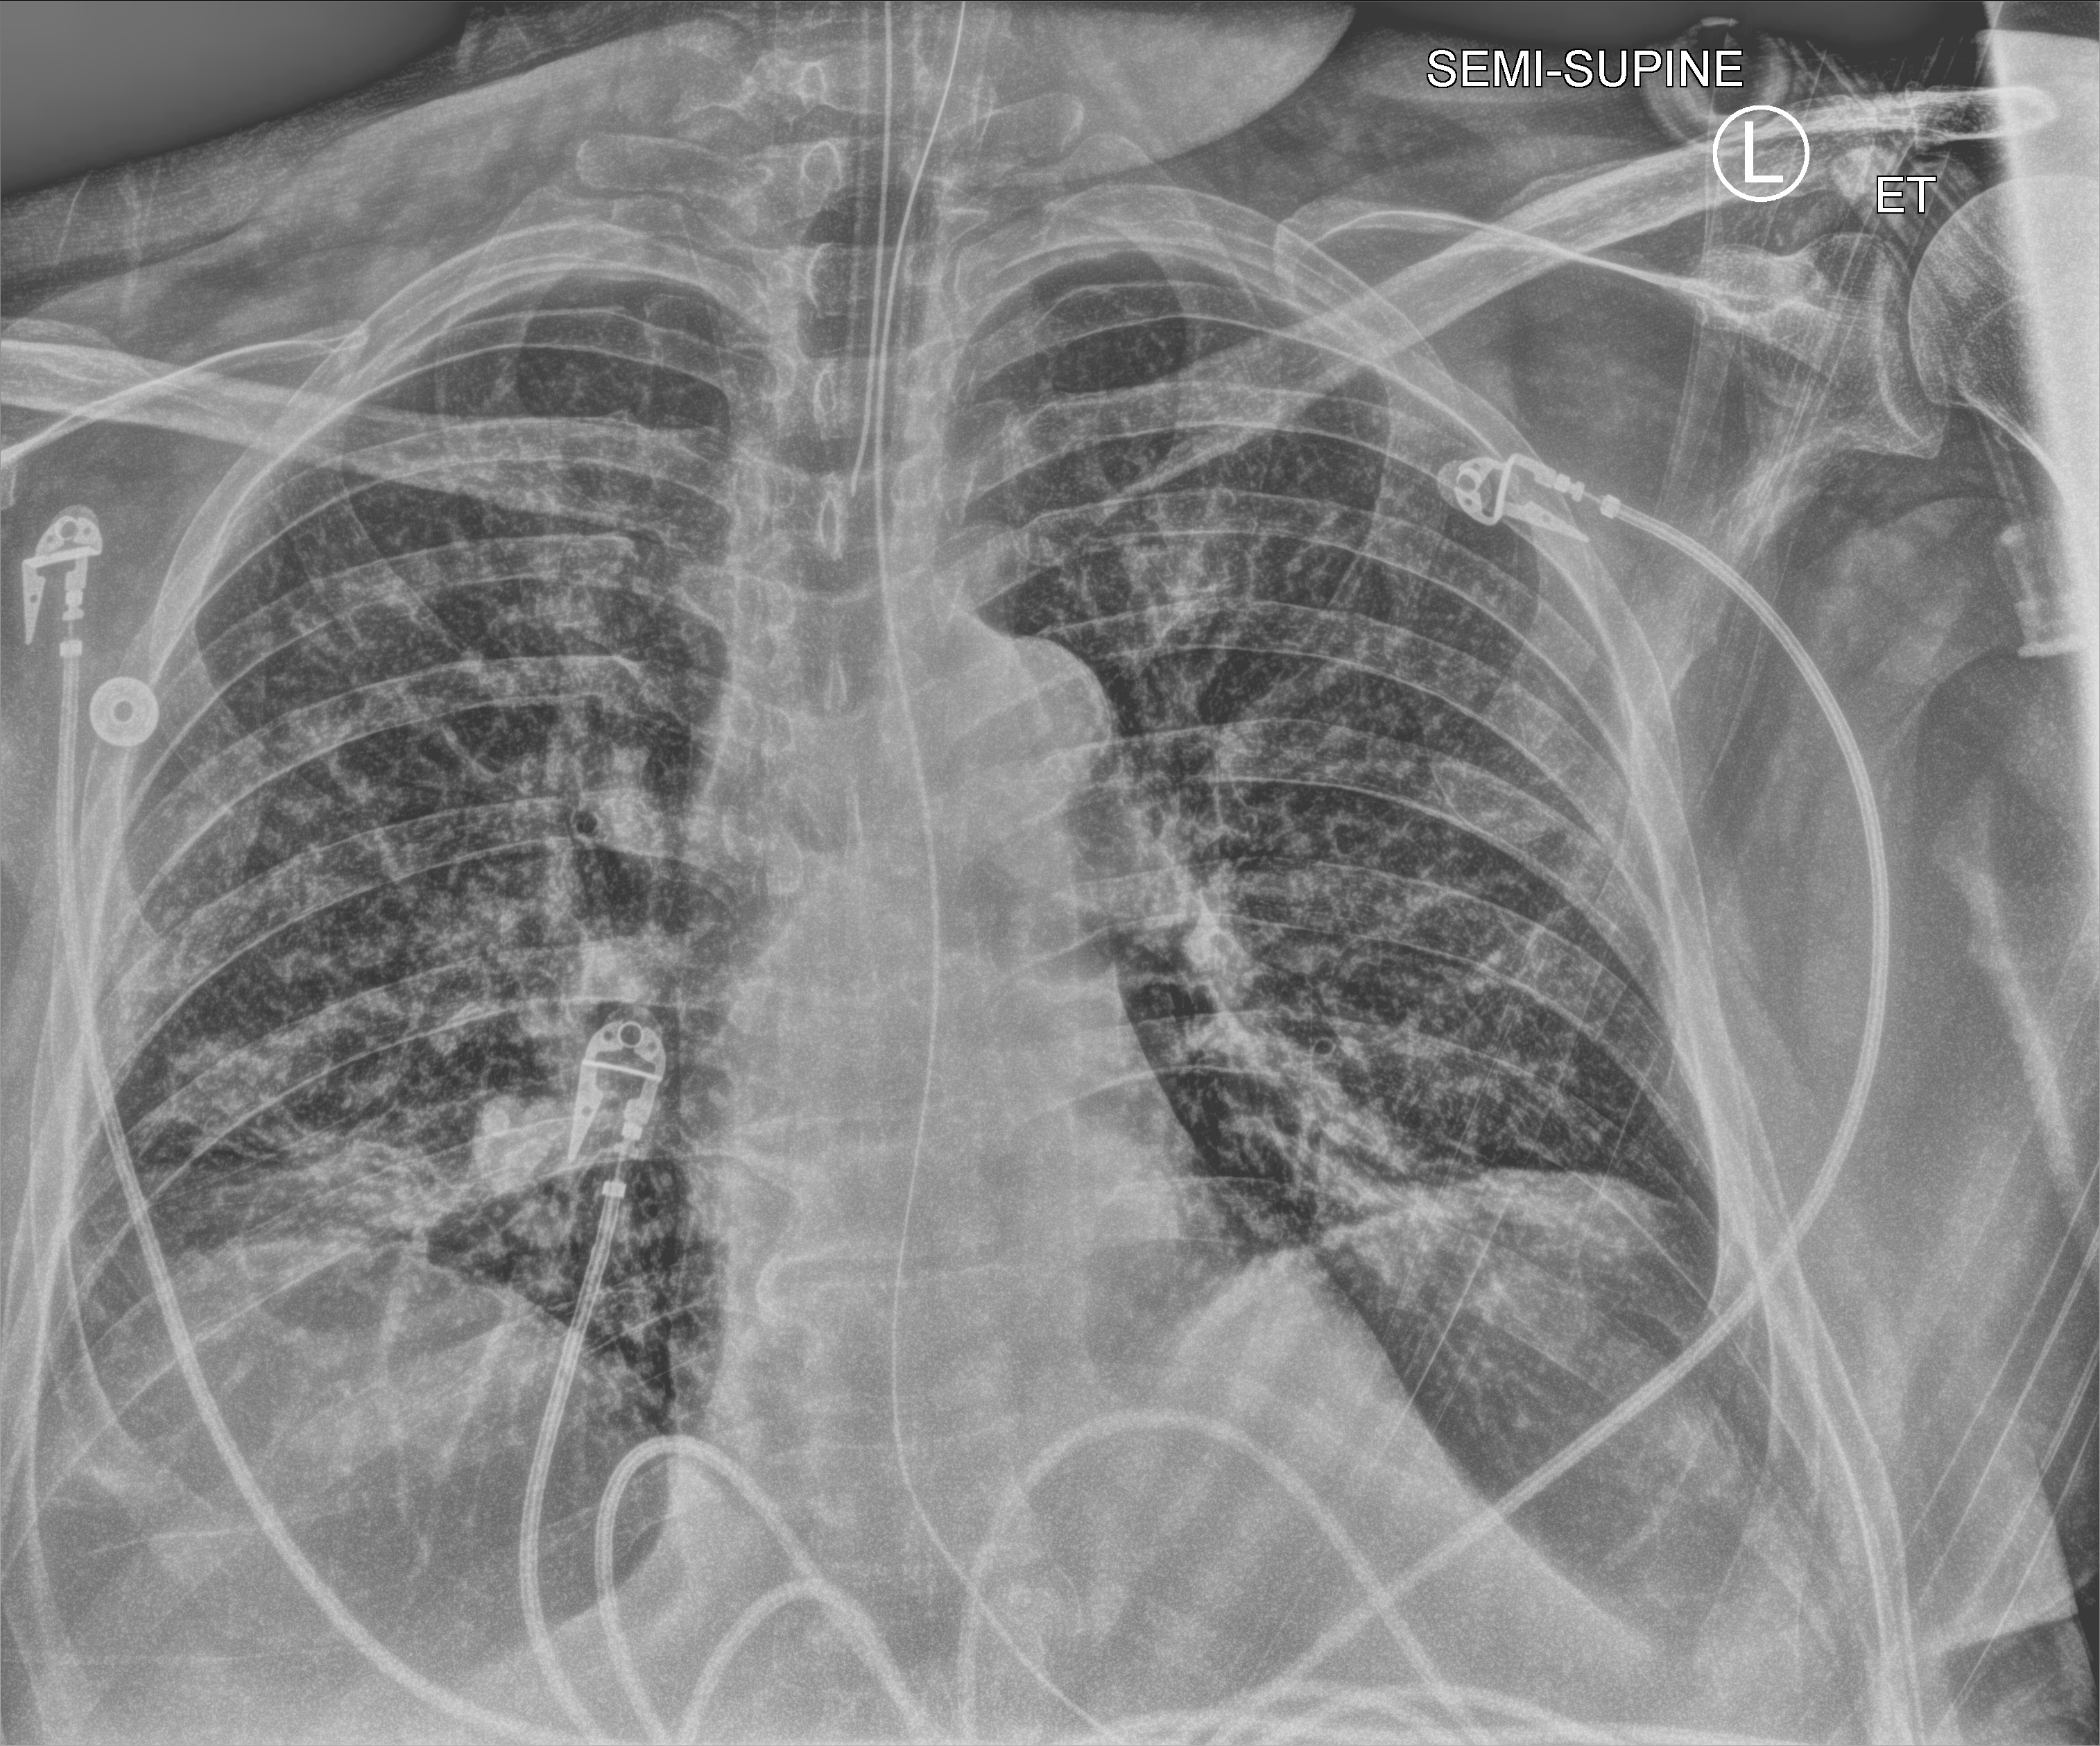
Bedside chest radiograph (computed radiography), anteroposterior (AP) projection. Male patient hospitalised with COVID-19, age 60–74 years.
Admission-level facts for this patient (not findings on this image; timing relative to this image not recorded):
- mechanically ventilated during this hospital stay: yes
- admitted to intensive care during this hospital stay: yes